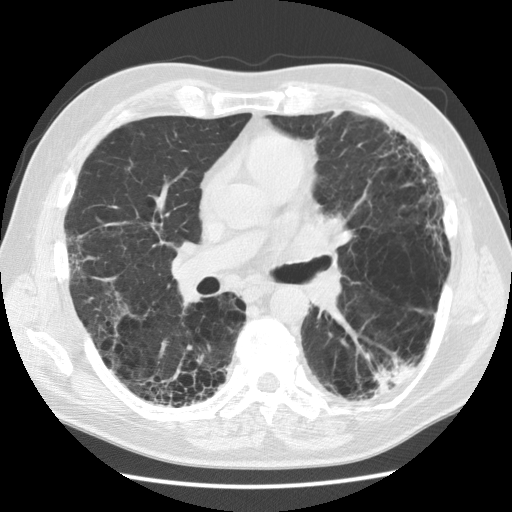
Low-dose screening chest CT, one axial slice. Position 68 of 128 along the scan axis. Reconstruction kernel STANDARD. 120 kVp. Lung window (W 1500 / L -600 HU). 512 × 512 image matrix, field of view 360 × 360 mm.
Annotated regions visible in this slice (manually delineated by an expert):
- lesion 1 (tumor, lower lobe of left lung): bounding box (x1, y1, x2, y2) in pixels: (374, 366, 414, 394)